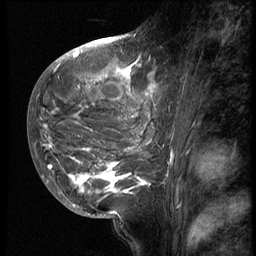
Breast MRI (dynamic contrast-enhanced), one sagittal slice; position 24 of 62 along the scan axis; 3 images stored at this slice position (order not interpretable as contrast timing); 1.5 T; TE 4.2 ms, TR 9 ms; 256 × 256 image matrix, field of view 180 × 180 mm. Female patient, age 28 years. Case-level facts recorded for this patient, not image findings: setting: breast cancer imaged before/during neoadjuvant chemotherapy.
Structures marked on this image (semi-automatic segmentation, software-assisted and operator-edited):
- analysis volume of interest (the breast-tissue region the enhancement analysis was run in; not a lesion): bounding box <42,45,167,207> (left, top, right, bottom; pixels)
- tumour enhancement mask (voxels above the 140 % enhancement threshold inside the analysis volume of interest): <42,45,159,196>